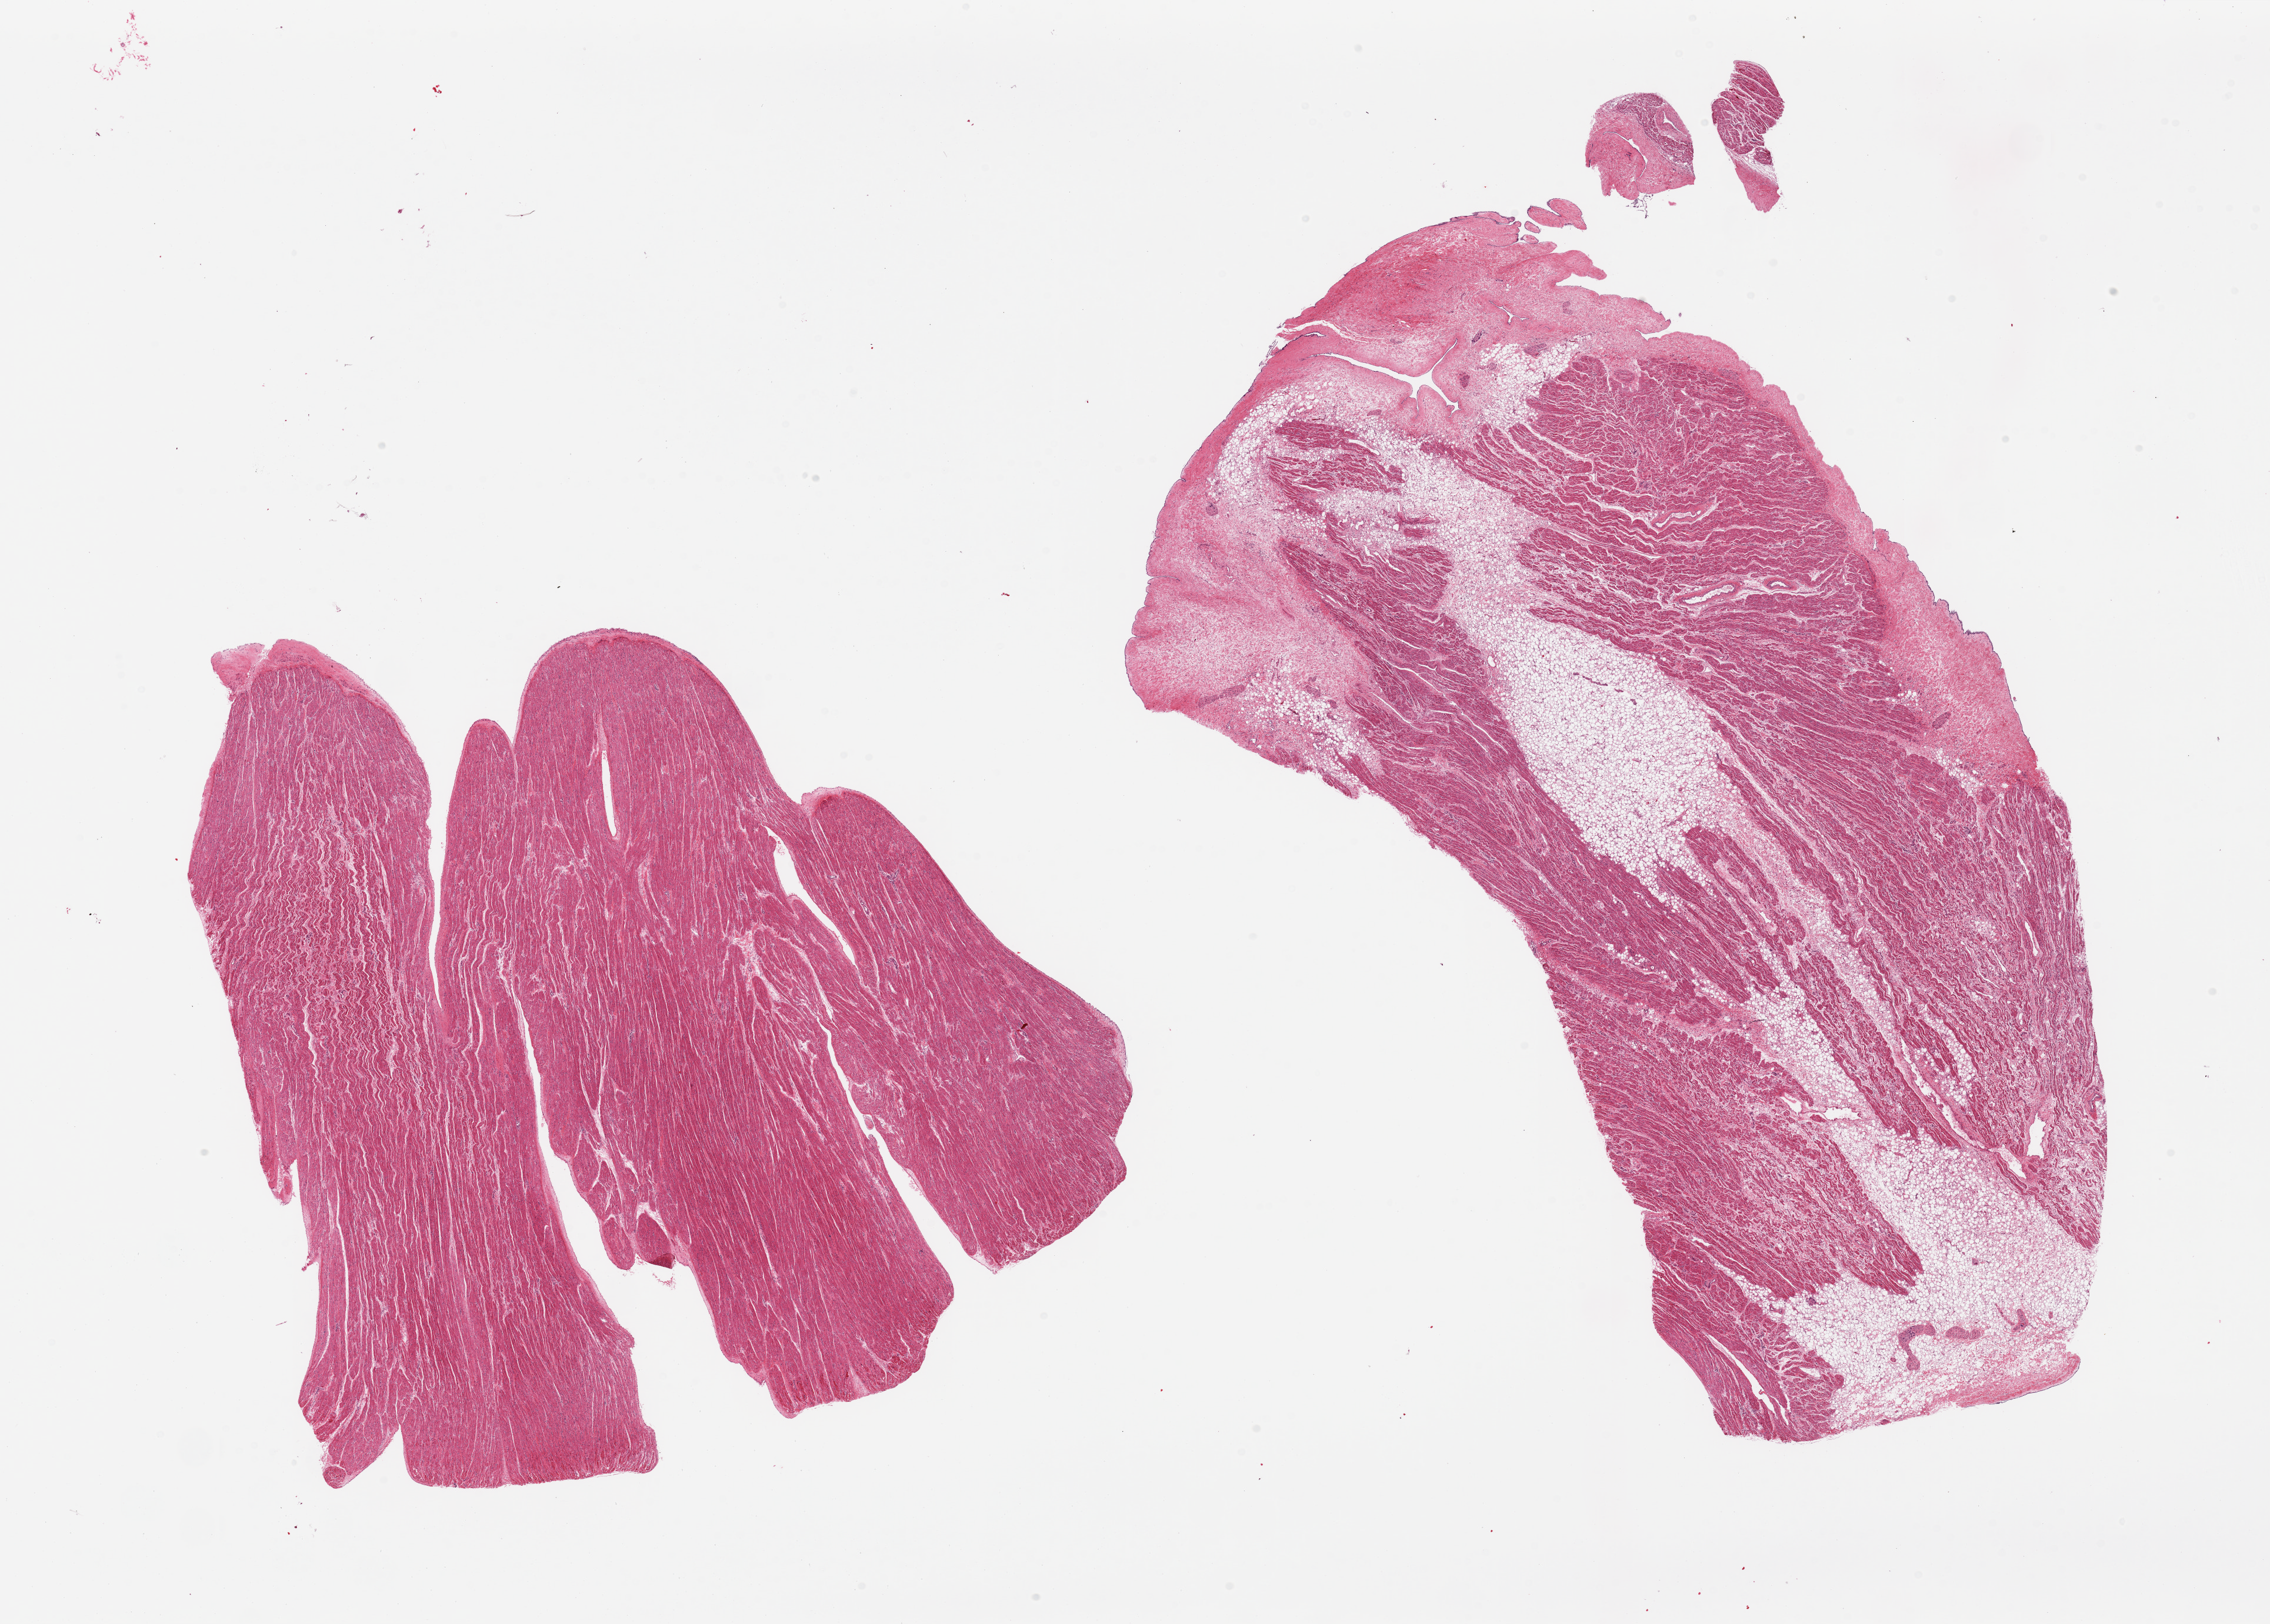
Digitized haematoxylin and eosin-stained section — shown as a low-resolution overview of the whole scanned area (about 30.5 x 21.8 mm, acquisition: 20x scan). PAXgene-fixed, paraffin-embedded tissue. Sampled site (target tissue): auricular appendage. Donor tissue sample. Donor sex: female.
• review note (as recorded): 2 pieces, 25% internal fat